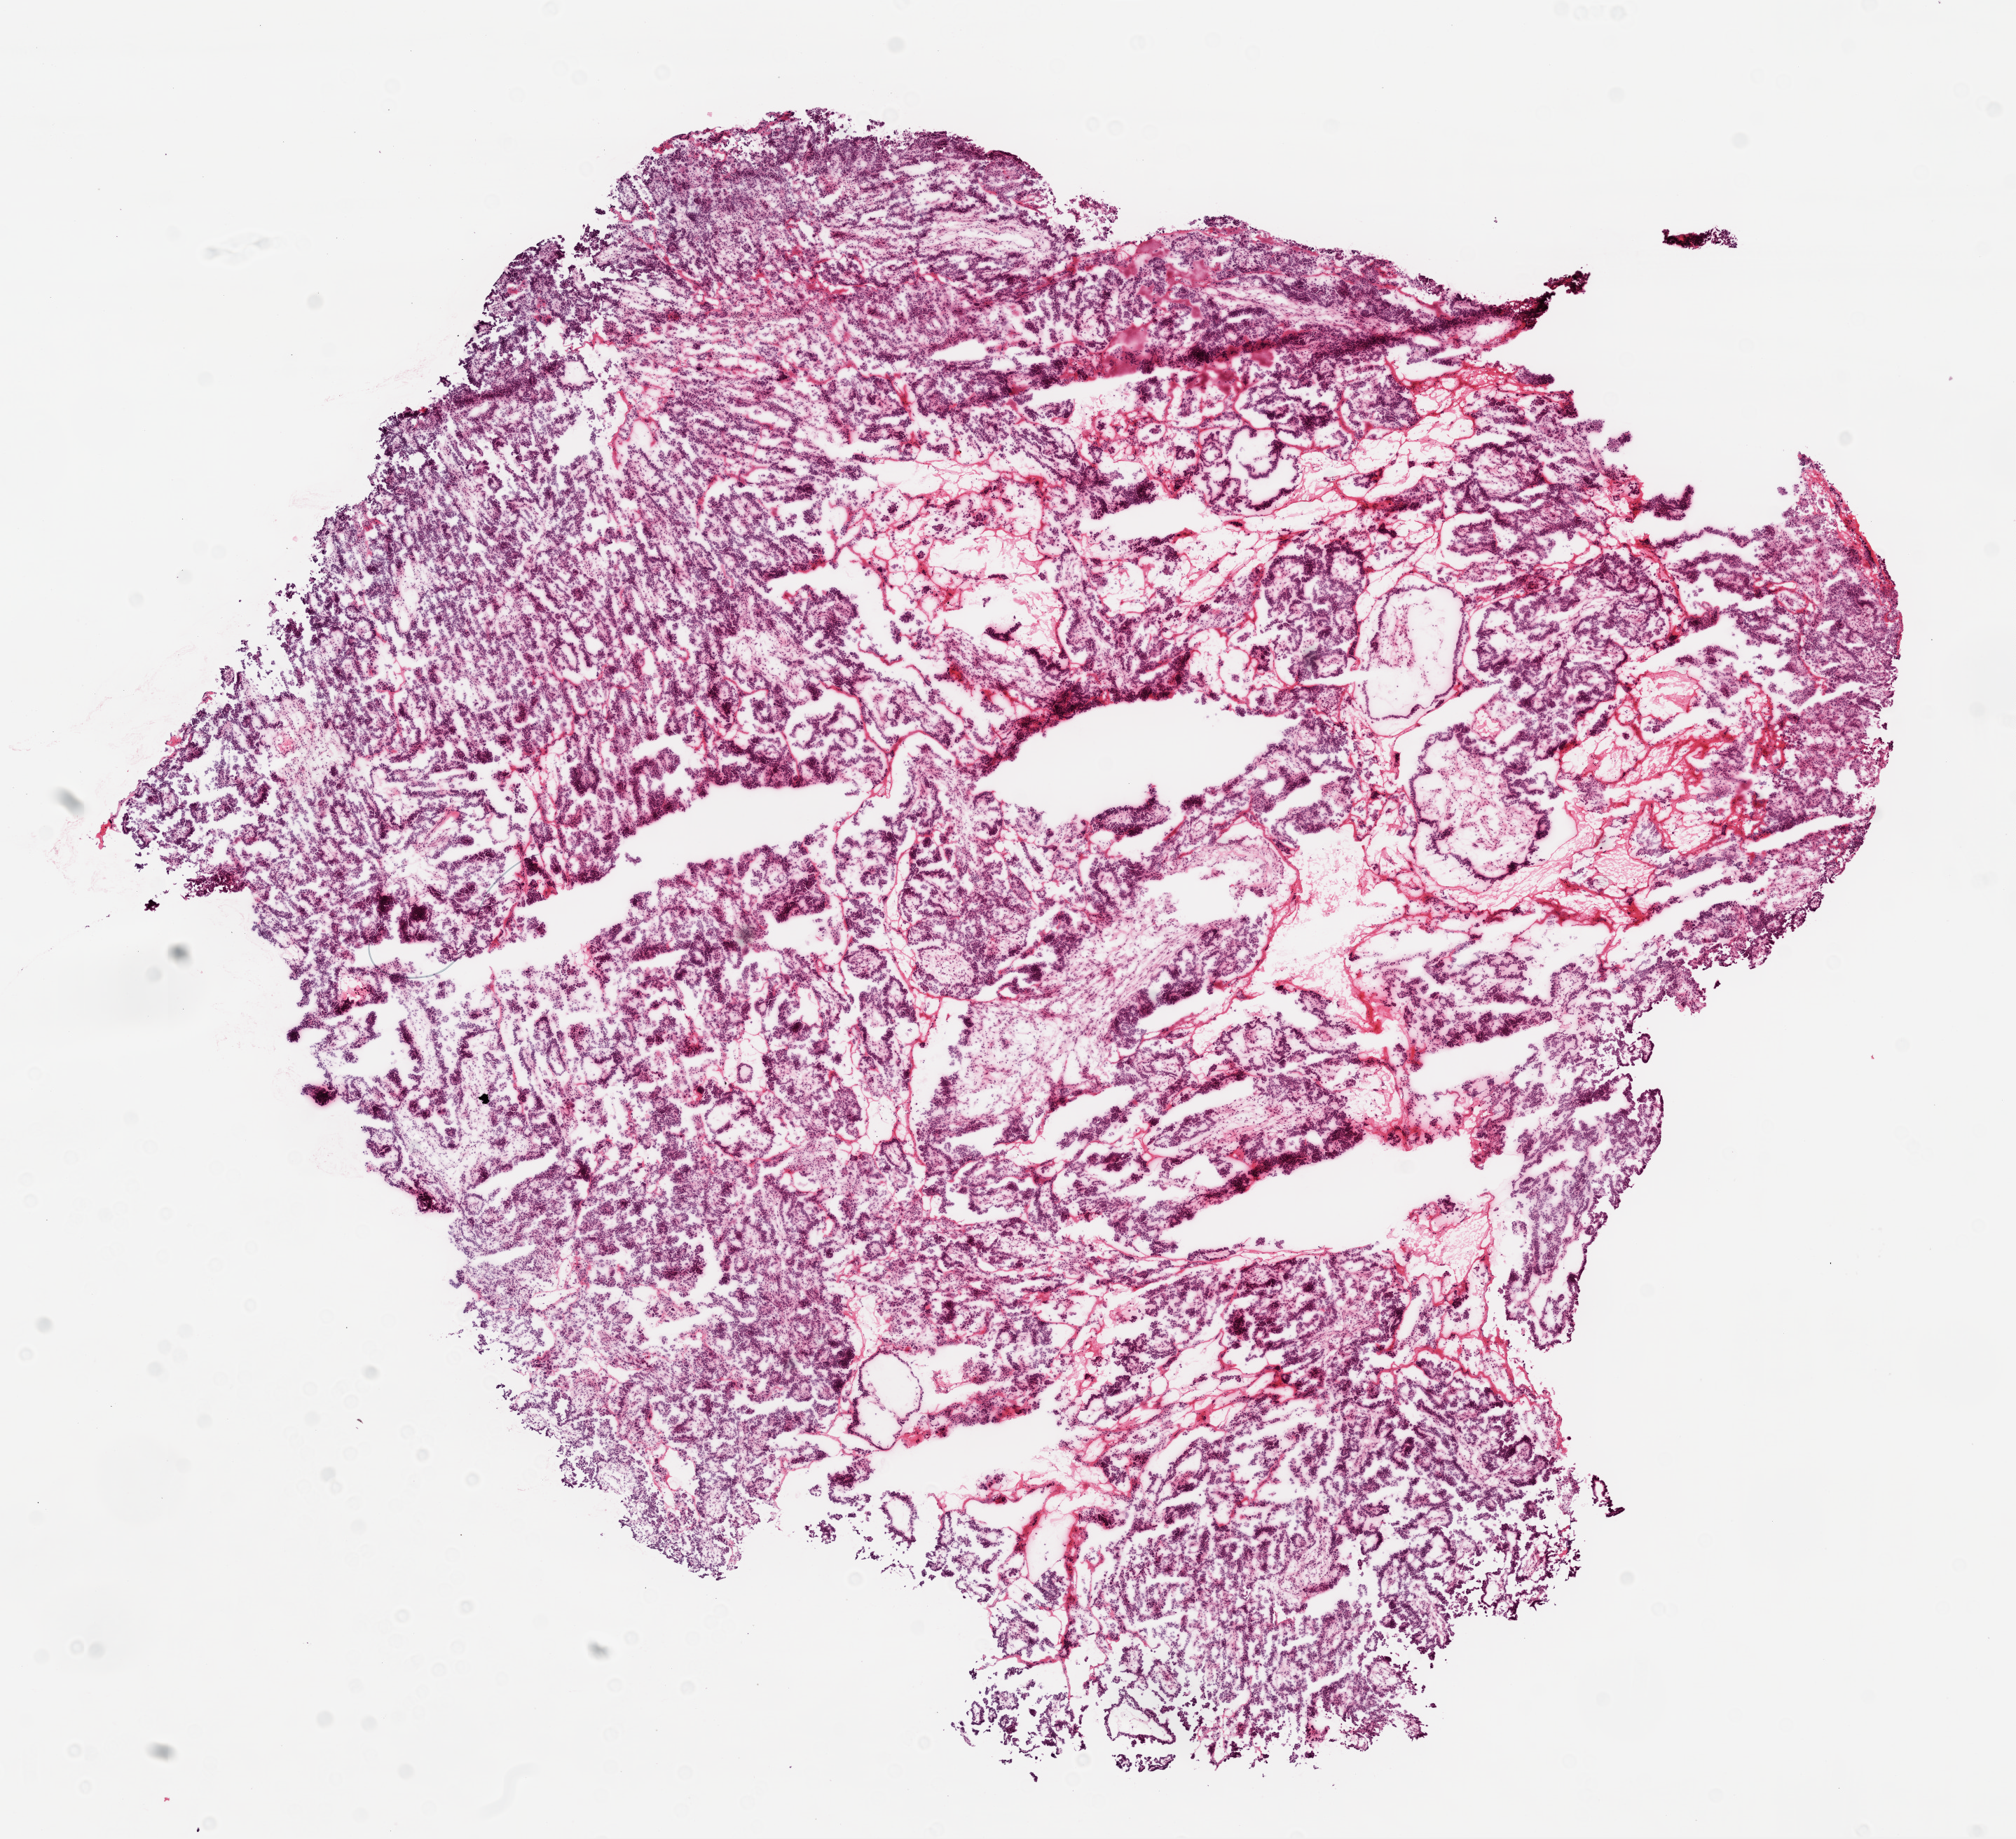
Digitized H&E tissue section (whole slide), a low-resolution overview of the entire scanned area, about 11.6 x 10.6 mm, frozen section from the top of the tissue portion, sample: primary tumour, ovary. Female, age 51 years at initial diagnosis.
Diagnosis: Serous cystadenocarcinoma, NOS.